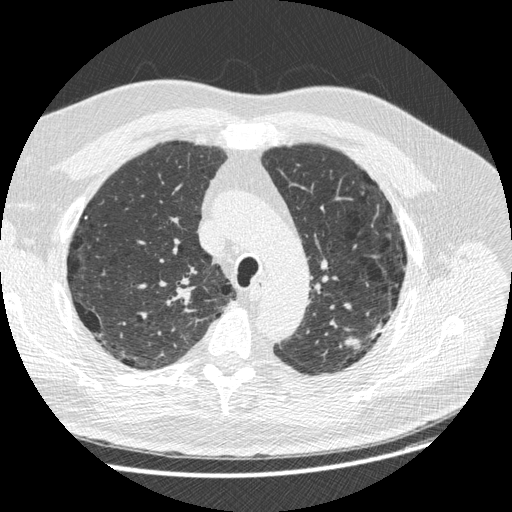
Low-dose screening chest CT, one axial slice; position 195 of 258 along the scan axis; 120 kVp; lung window (W 1500 / L -600 HU); 1.25 mm slice thickness; 512 × 512 image matrix.
Annotated regions visible in this slice (manually delineated by an expert):
- lesion 1 (tumor, upper lobe of left lung): bounding box (x1, y1, x2, y2) in pixels: (345, 337, 361, 349)